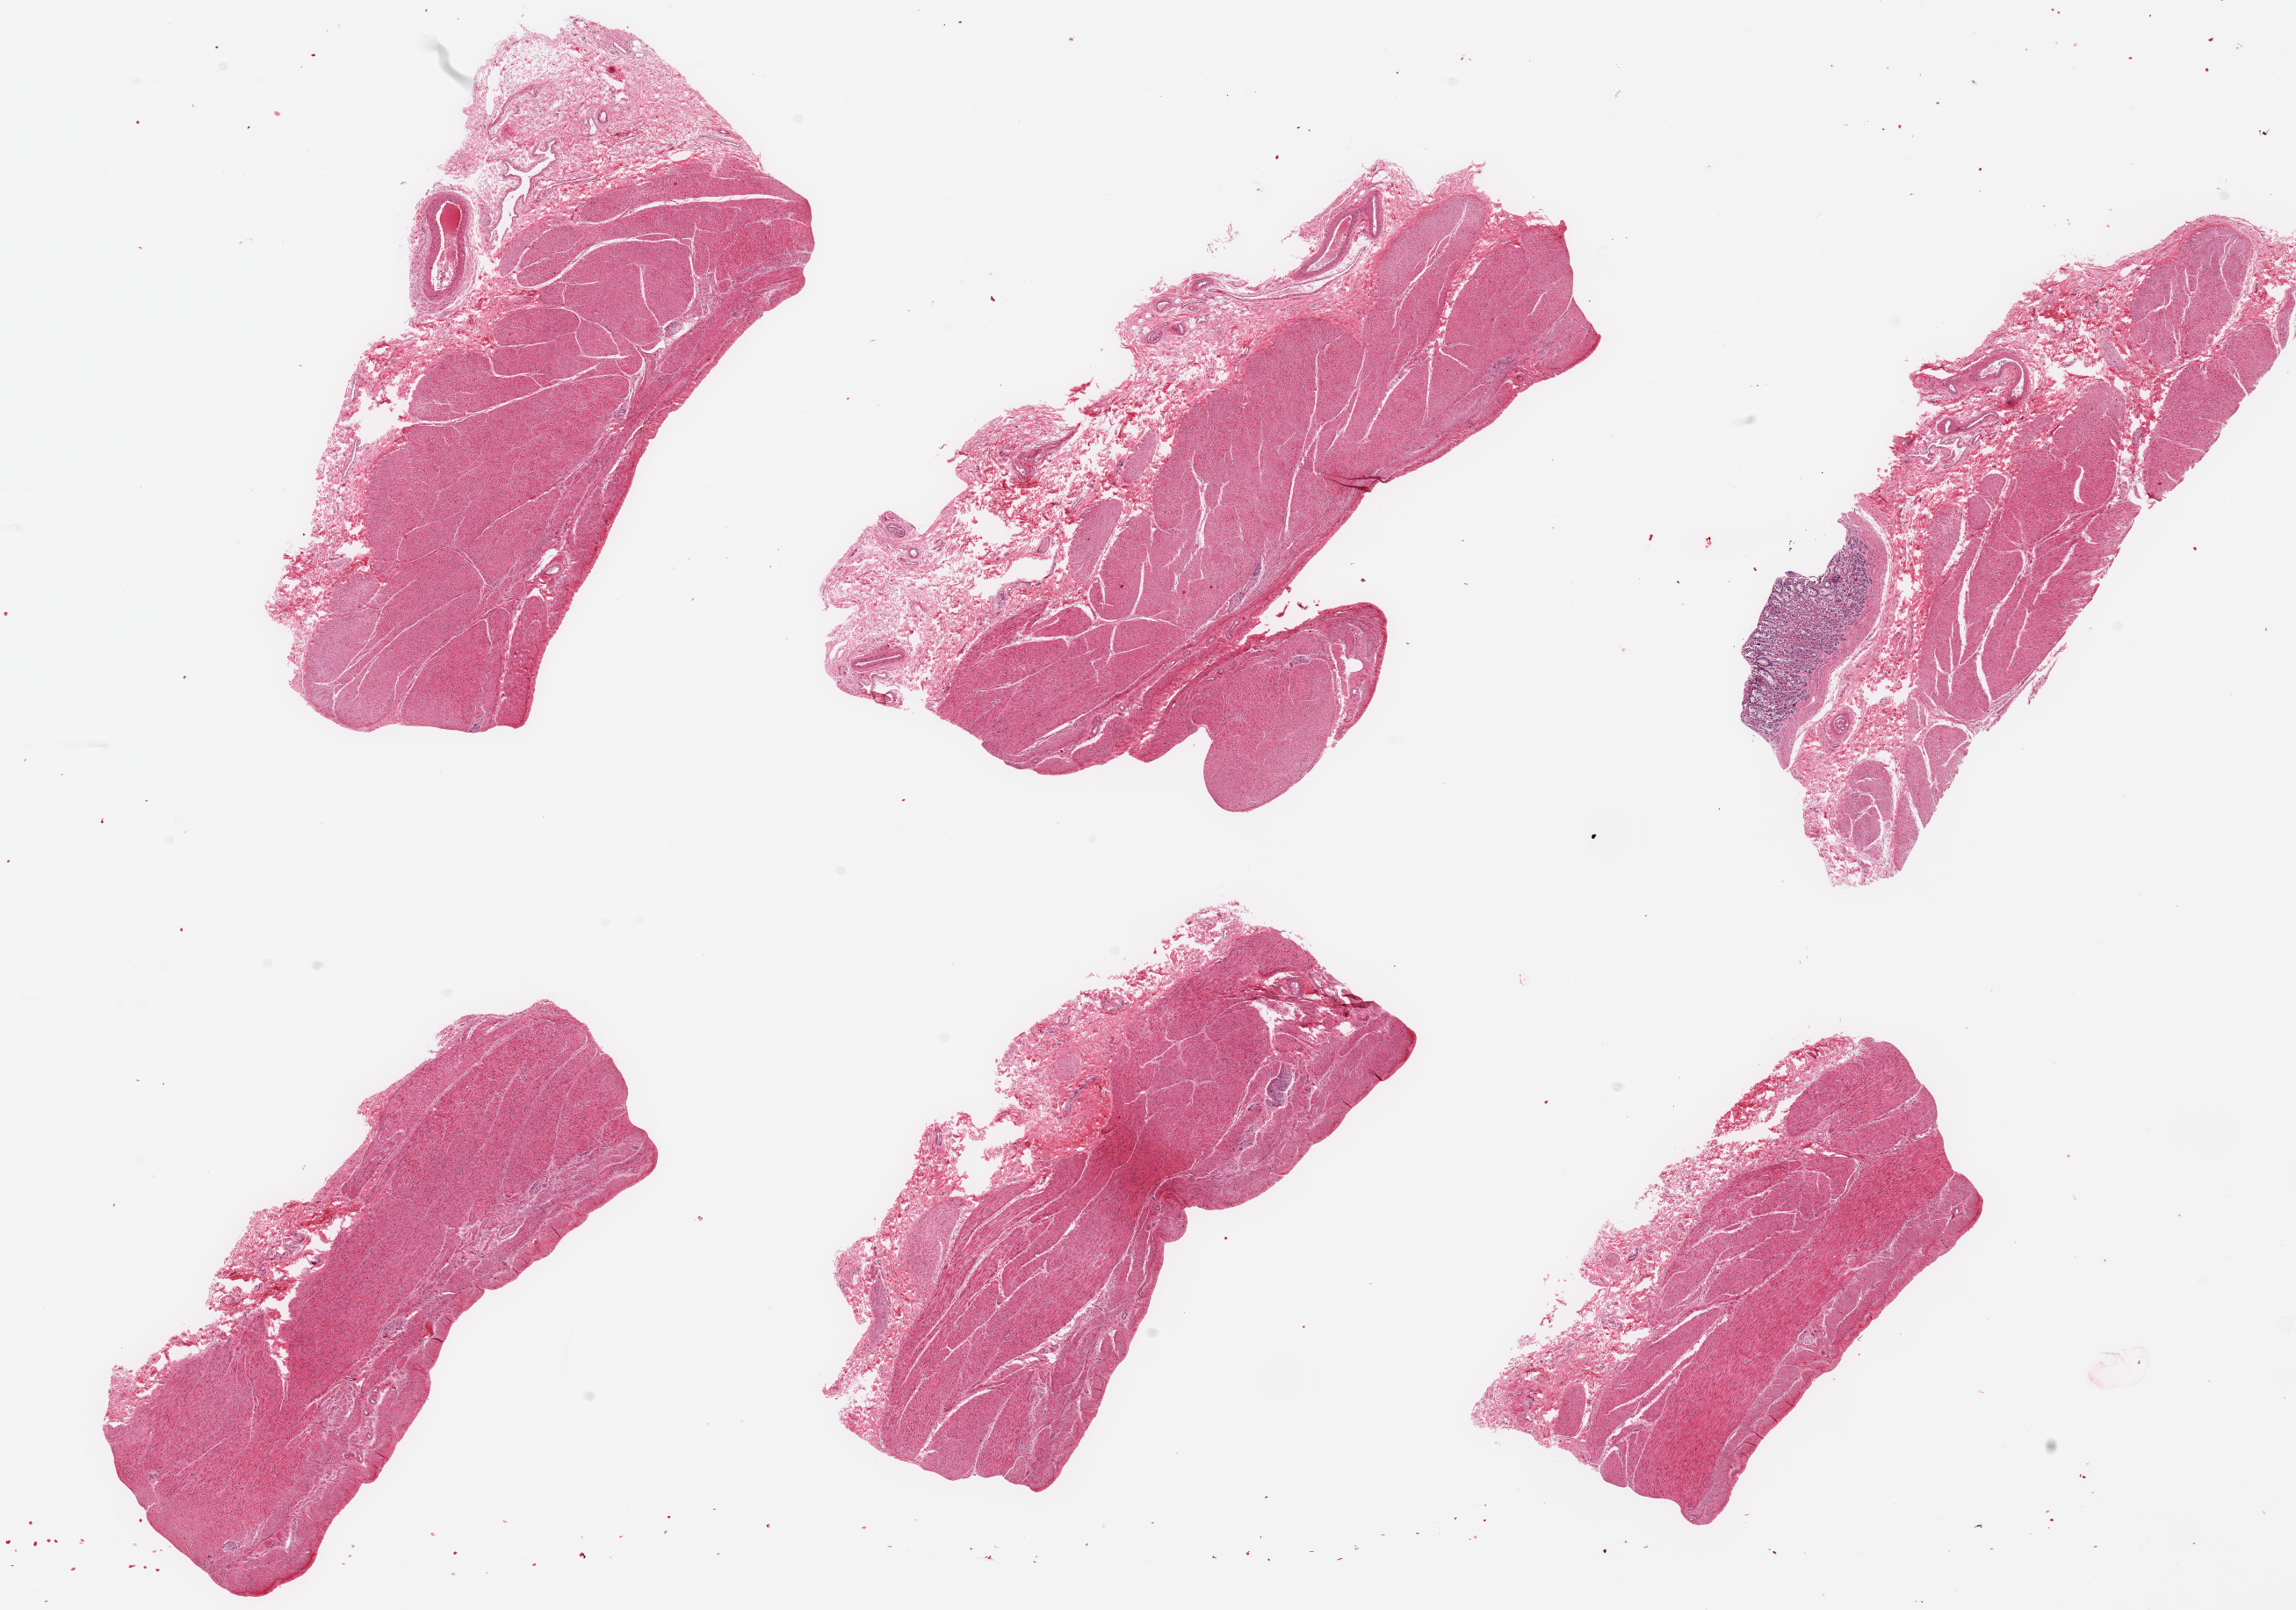
Hematoxylin and eosin (H&E) whole-slide image, brightfield — low-resolution overview of the scanned area, about 20.7 x 14.5 mm, PAXgene-fixed, paraffin-embedded tissue, section of stomach (target tissue), donor tissue sample. Donor: male.
• pathologist's review note for this sample: 6 pieces; one of 6 samples contains a tiny fragment of gastric mucosa; all samples comprised of muscularis and attached up to 1.5mm adventitia